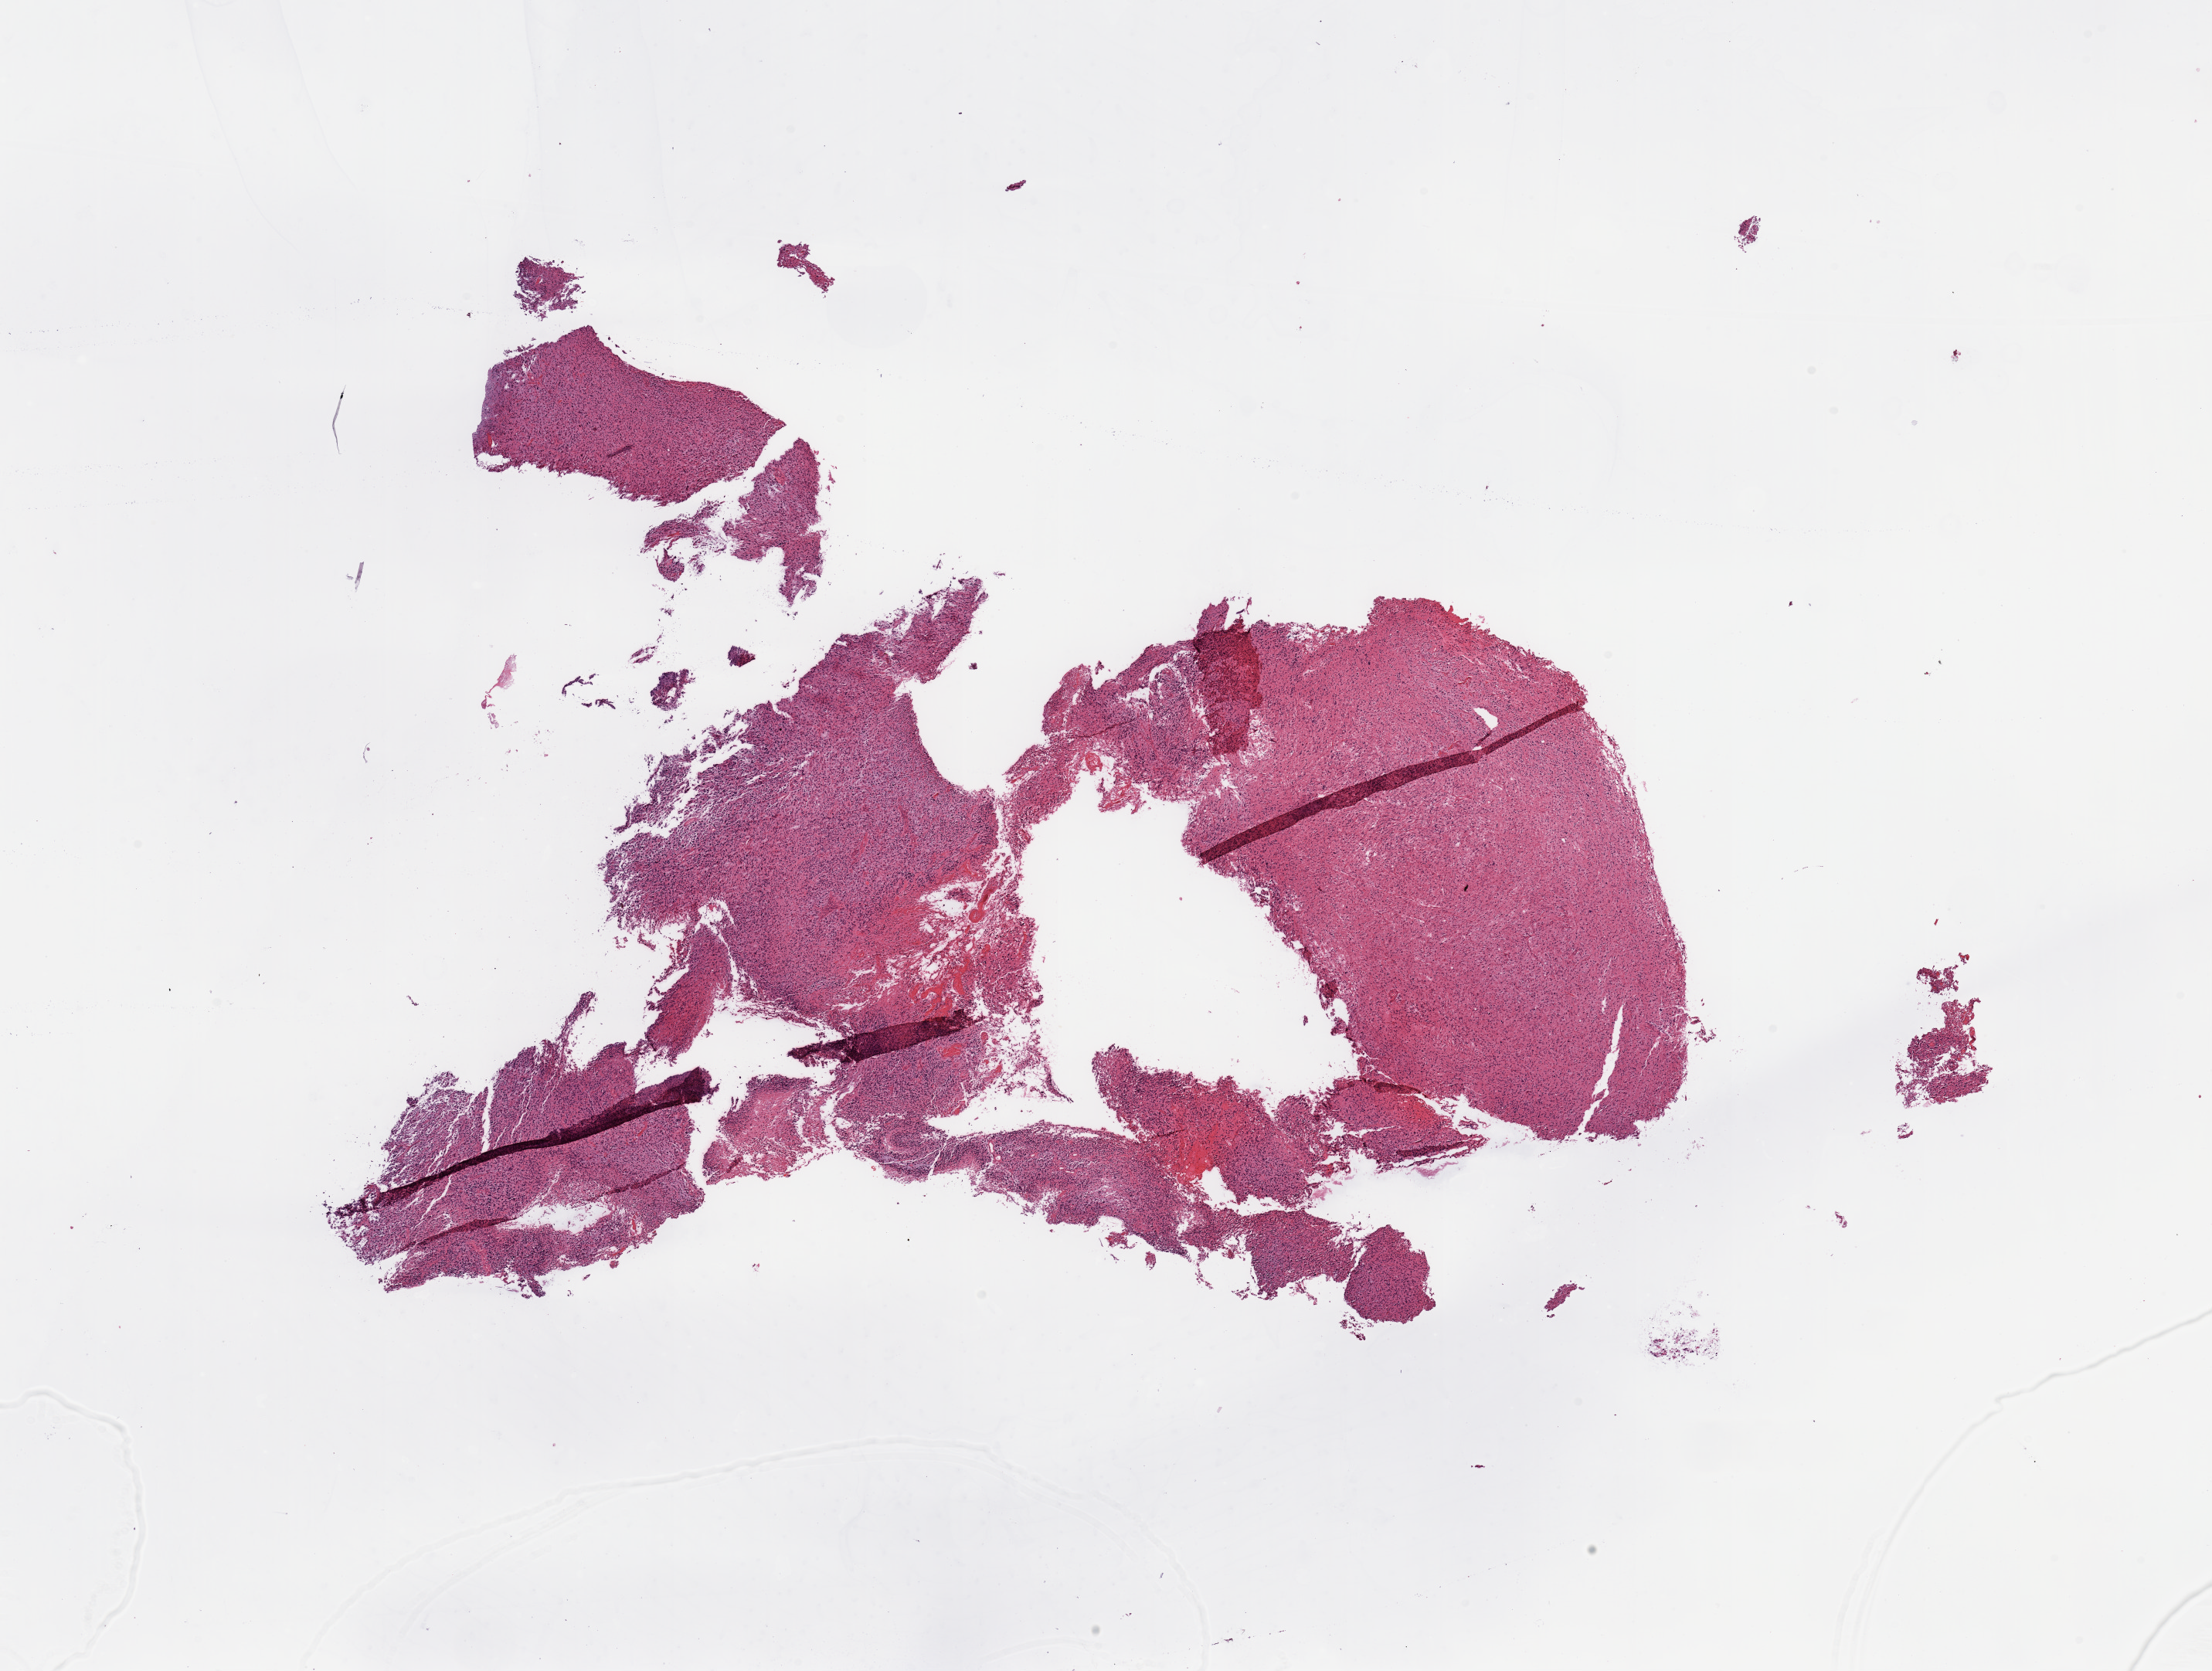
Digitized Hematoxylin and eosin (H&E) stained tissue section (whole slide), low-resolution overview of the scanned area, about 22.6 x 17.1 mm (acquisition: 20x scan). Tumour tissue sample, brain. 70-year-old male patient.
• primary tumour site (as recorded): parietal lobe
• patient diagnosis (cohort enrolment): glioblastoma multiforme (brain)